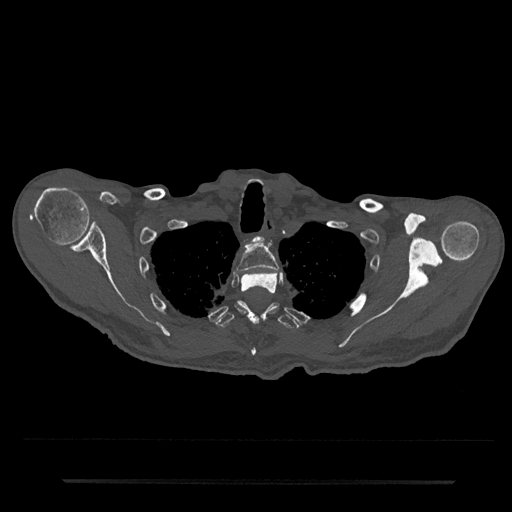
CT including the spine, one axial slice; slice 654 of 797 in the series (ordered by position); 120 kVp; bone window (W 1800 / L 400 HU); 0.5 mm slice thickness; 512 × 512 image matrix, field of view 427 × 427 mm. Male patient, age 74 years. From the clinical record (not read from this slice): primary cancer: prostate.
Annotated regions visible in this slice (semi-automatic segmentation, software-assisted and operator-edited):
- T1 vertebra: bounding box (x1, y1, x2, y2) in pixels: (259, 236, 263, 240)
- T2 vertebra: (236, 243, 279, 273)
- T3 vertebra: (238, 273, 277, 356)
- T4 vertebra: (216, 301, 300, 329)